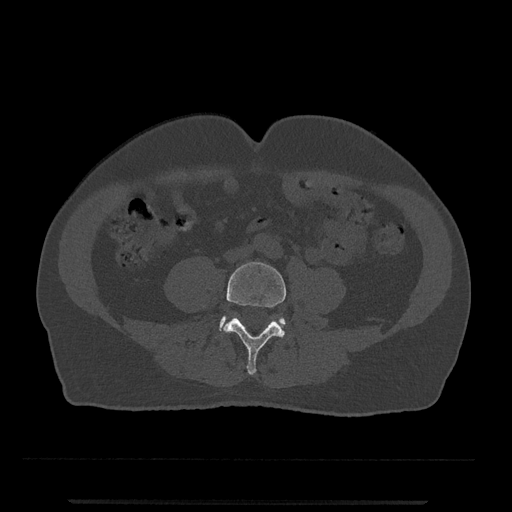
CT including the spine, one axial slice. Slice 123 of 797 in the series (ordered by position). Reconstruction kernel Br40s/3. 120 kVp. Bone window (W 1800 / L 400 HU). 512 × 512 image matrix, field of view 419 × 419 mm. Patient: male, 63 years. From the clinical record (not read from this slice): primary cancer: prostate.
Structures marked on this image (semi-automatically segmented with operator editing):
- L4 vertebra: box from (x=223, y=262) to (x=286, y=375) px
- L5 vertebra: (x=219, y=316)–(x=286, y=331)